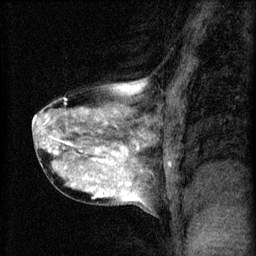
Breast MRI (dynamic contrast-enhanced), one sagittal slice. Slice 30 of 60 in the series (ordered by position). 3 images stored at this slice position (order not interpretable as contrast timing). 1.5 T. TE 4.2 ms, TR 8.2 ms. 2 mm slice thickness. 256 × 256 image matrix, field of view 180 × 180 mm. Patient: female, 40 years.
Annotated regions visible in this slice (semi-automatically segmented with operator editing):
- analysis volume of interest (the breast-tissue region the enhancement analysis was run in; not a lesion): bounding box (x1, y1, x2, y2) in pixels: (31, 80, 167, 211)
- tumour enhancement mask (voxels above the 70 % enhancement threshold inside the analysis volume of interest): (34, 90, 135, 199)